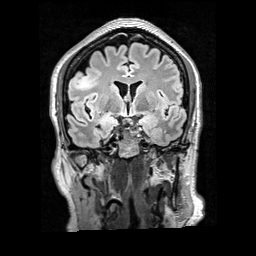
Brain MRI from a brain-tumour surgery series, one coronal slice; slice 112 of 200 in the series (ordered by position); T2 FLAIR; 1 mm slice thickness; 256 × 256 image matrix, field of view 256 × 256 mm. Case-level facts recorded for this patient, not image findings: histopathology: Glioblastoma; WHO grade: 4; IDH mutation: no.
Annotated regions visible in this slice (manually delineated by an expert):
- tumour: bounding box <73,71,102,91> (left, top, right, bottom; pixels)